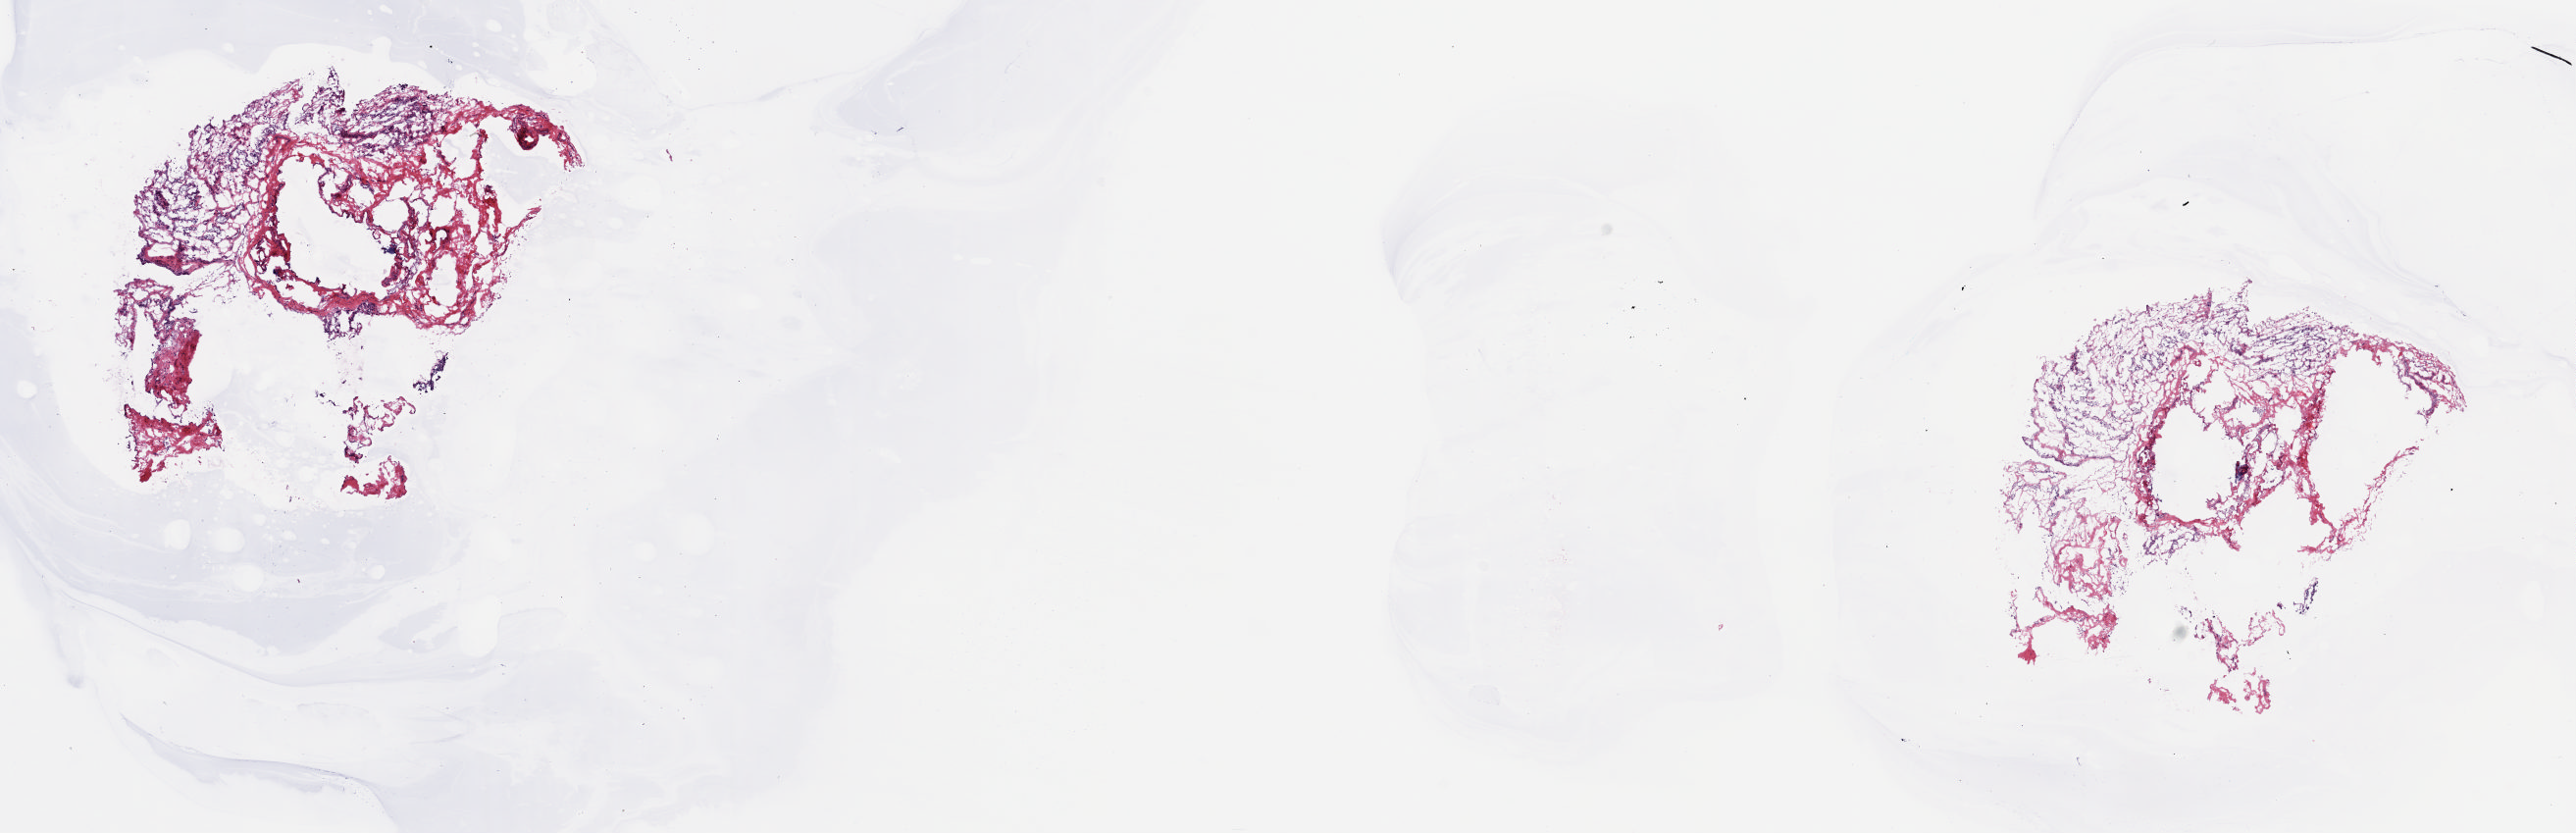
H&E whole-slide image, low-resolution overview of the scanned area, about 20.8 x 6.7 mm (slide scanned at 20x), frozen section, thymus, solid tissue normal (non-tumour tissue) sample. Male patient; age at initial diagnosis 45 years.
This section: solid tissue normal (non-tumour) sample from the same patient. Patient diagnosis: Thymoma, type B1, malignant.